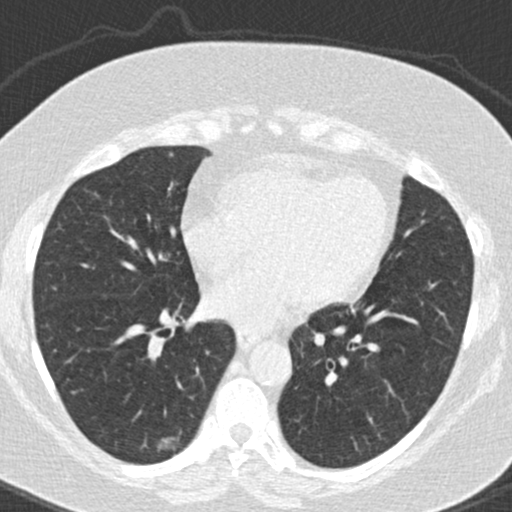
Low-dose screening chest CT, one axial slice. Position 74 of 177 along the scan axis. 120 kVp. Lung window (W 1500 / L -600 HU). 2 mm slice thickness. 512 × 512 image matrix, field of view 300 × 300 mm.
Annotated regions visible in this slice (outlined manually by an expert reader):
- lesion 1 (tumor, lower lobe of right lung): box from (x=158, y=437) to (x=178, y=450) px